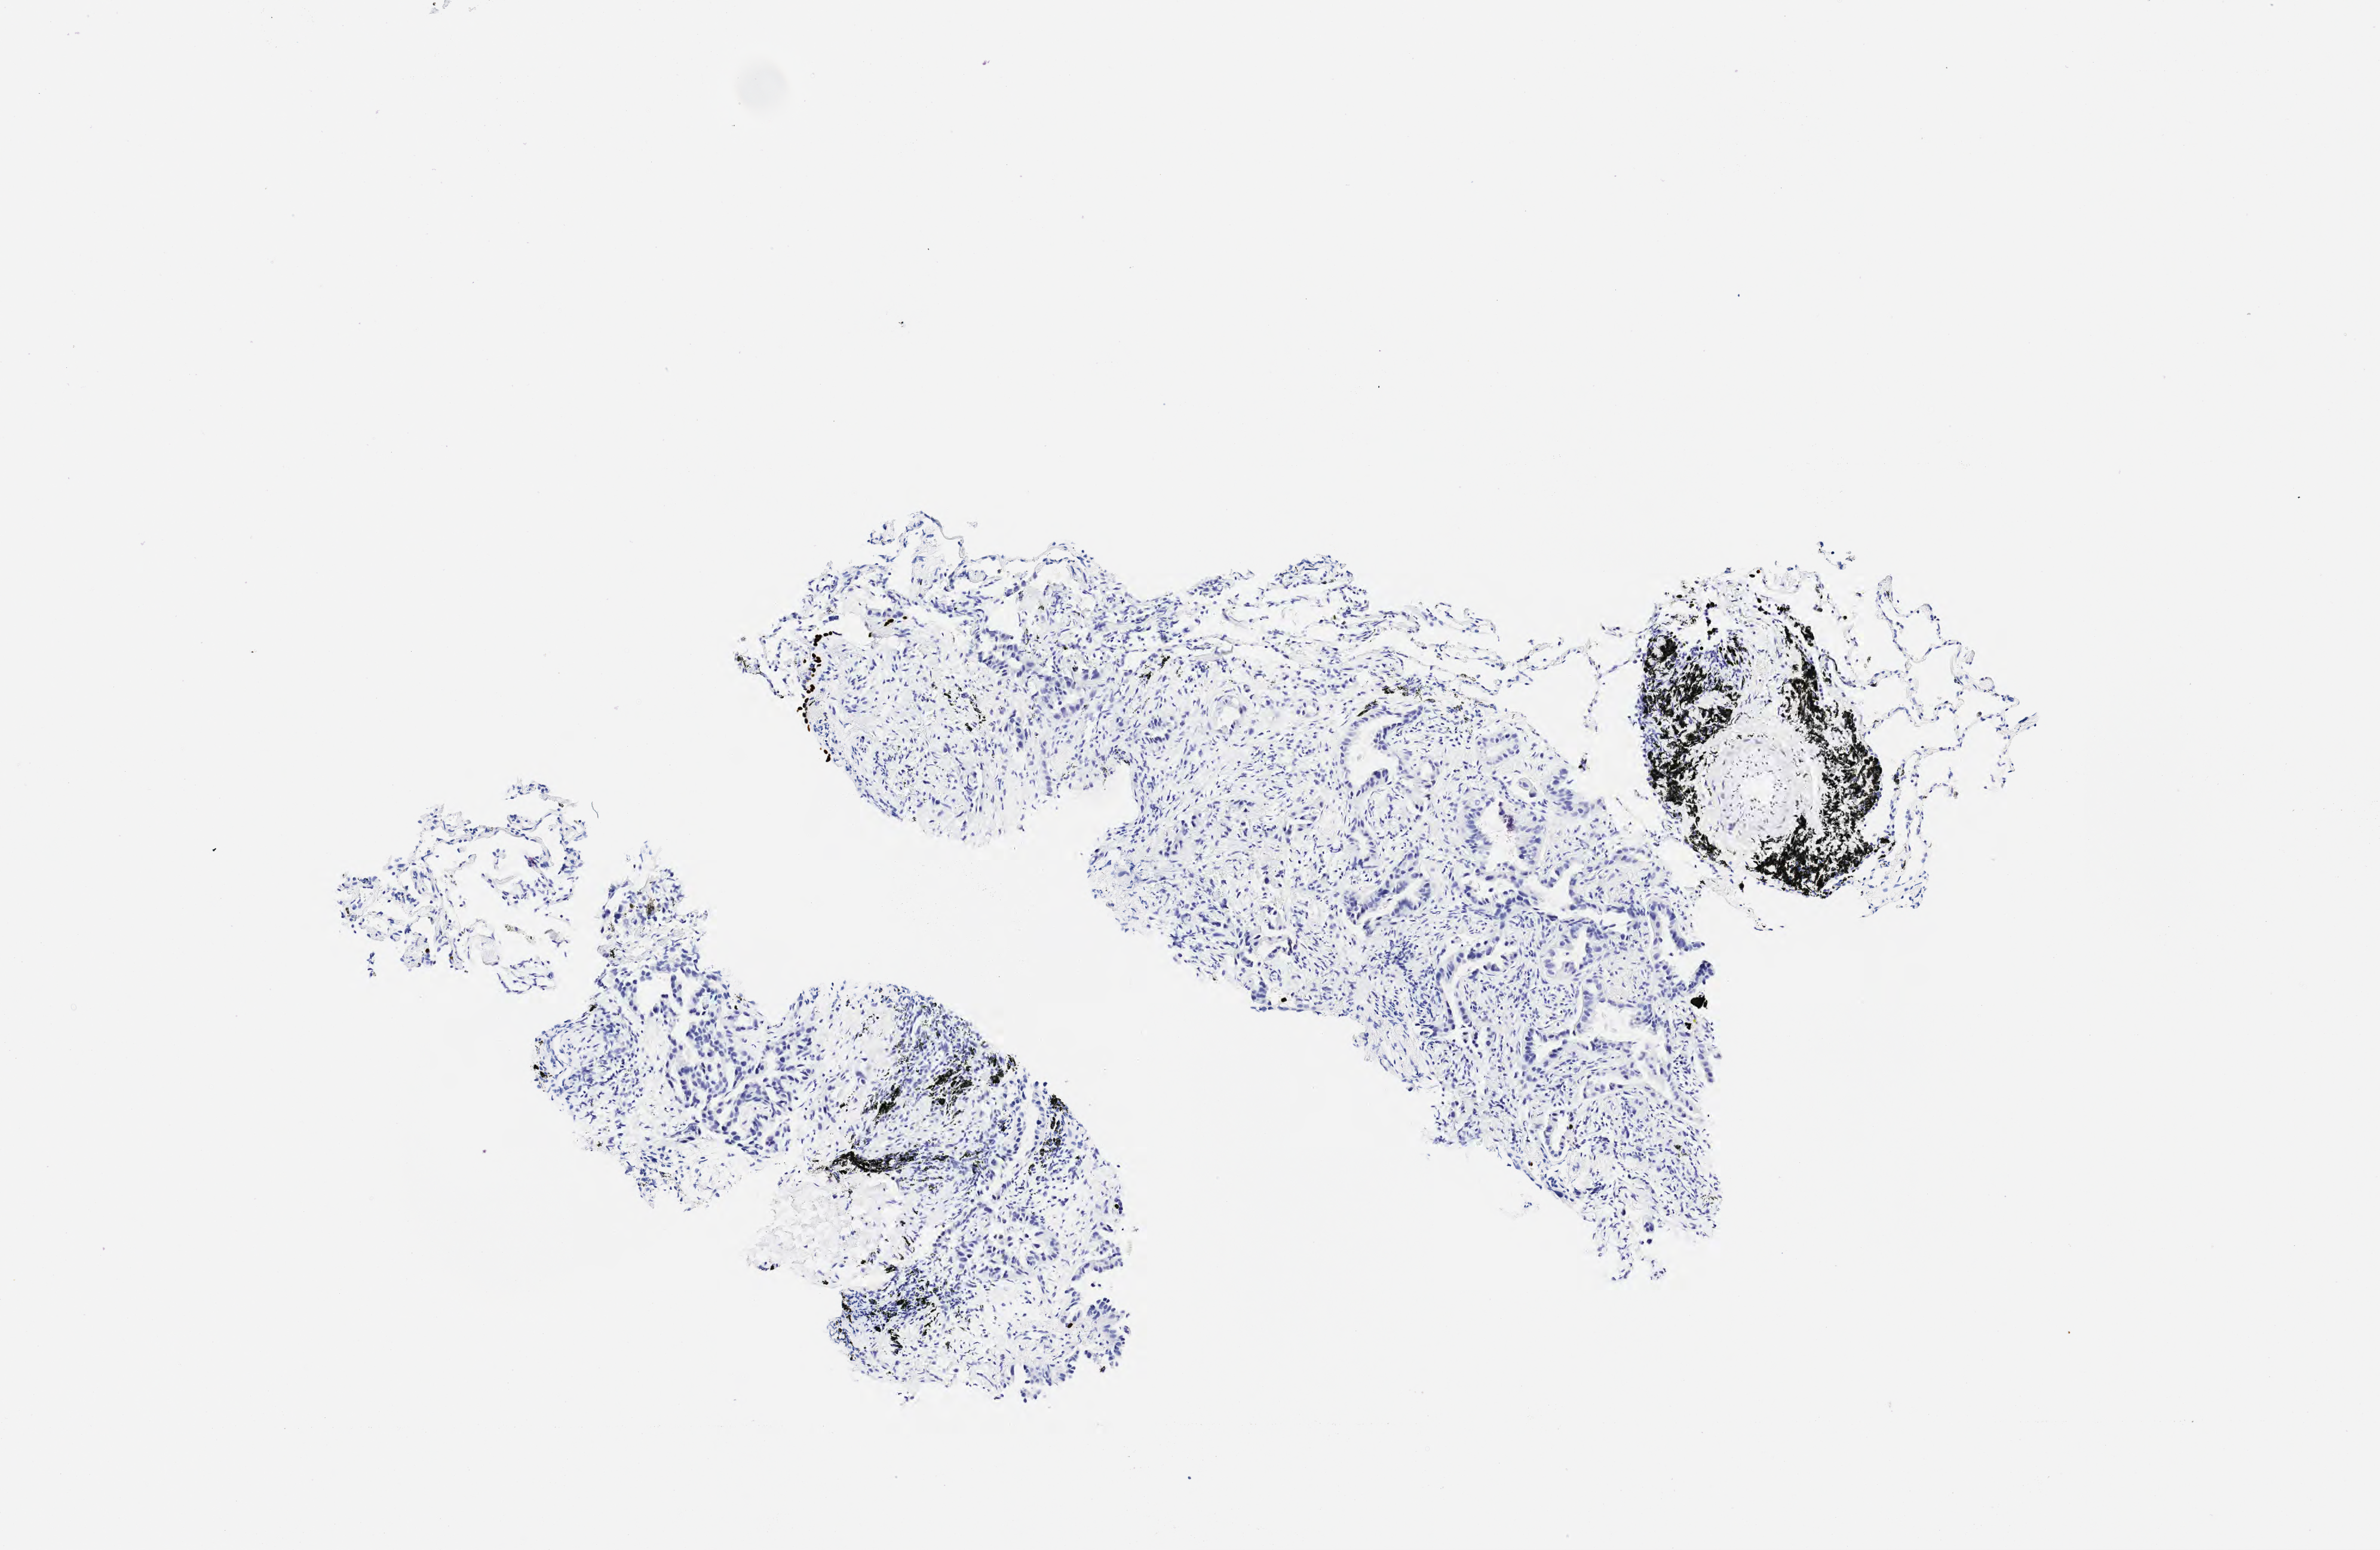
Whole-slide image, immunohistochemical stain for p40 — low-resolution overview of the scanned area, about 4.0 x 2.6 mm, tumor tissue, anatomic site: lung (left). Patient female; 63 years old.
Diagnosis: Adenocarcinoma, NOS.